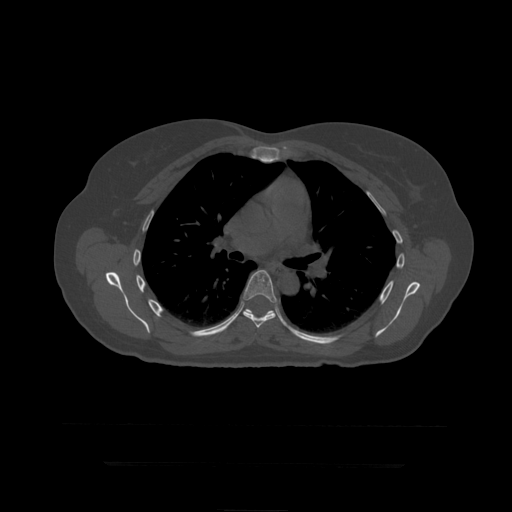
CT including the spine, one axial slice. Slice 298 of 399 in the series (ordered by position). 120 kVp. Bone window (W 1800 / L 400 HU). 1.25 mm slice thickness. 512 × 512 image matrix, field of view 450 × 450 mm. Patient age 41 years. Case-level facts recorded for this patient, not image findings: primary cancer: breast.
Structures marked on this image (semi-automatic segmentation, software-assisted and operator-edited):
- T7 vertebra: bounding box <243,270,278,328> (left, top, right, bottom; pixels)
- T8 vertebra: <245,309,273,313>